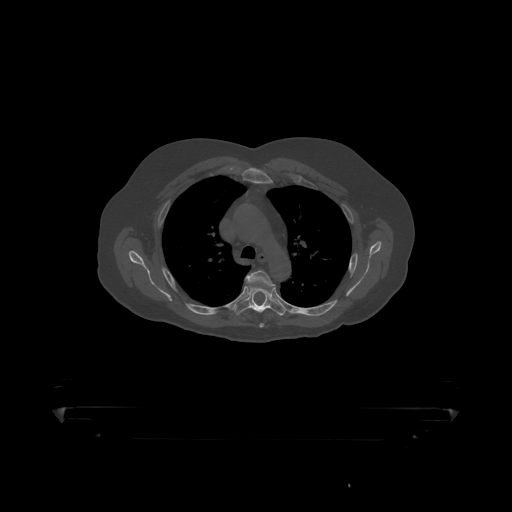
CT including the spine, one axial slice. Position 327 of 390 along the scan axis. Bone window (W 1800 / L 400 HU). 1.25 mm slice thickness. 512 × 512 image matrix, field of view 650 × 650 mm. Patient: male, 60 years. Case-level facts recorded for this patient, not image findings: primary cancer: prostate.
Annotated regions visible in this slice (semi-automatically segmented with operator editing):
- T4 vertebra: bounding box (x1, y1, x2, y2) in pixels: (246, 271, 275, 287)
- T5 vertebra: (233, 286, 287, 315)